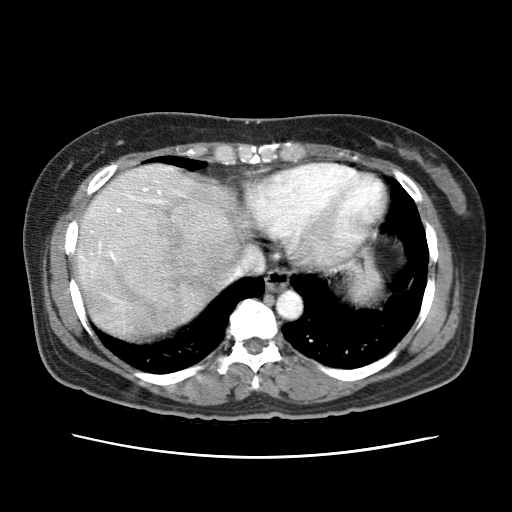
Contrast-enhanced abdominal CT (liver protocol), one axial slice; position 60 of 79 along the scan axis; reconstruction kernel STANDARD; 120 kVp; soft-tissue window (W 400 / L 40 HU); 2.5 mm slice thickness; 512 × 512 image matrix, field of view 340 × 340 mm. Case-level facts recorded for this patient, not image findings: diagnosis: hepatocellular carcinoma (patient treated with transarterial chemoembolisation; whether this scan precedes or follows treatment is not stated here); TNM stage (as recorded): Stage-I; Child-Pugh class: A.
Annotated regions visible in this slice (semi-automatically segmented with operator editing):
- abdominal aorta: bounding box (x1, y1, x2, y2) in pixels: (275, 290, 303, 318)
- liver parenchyma outside the tumour (the mass and vessels are separate outlines, so this box may not span the whole liver): (76, 164, 248, 336)
- mass: (109, 199, 239, 304)
- liver vessels: (81, 188, 162, 261)